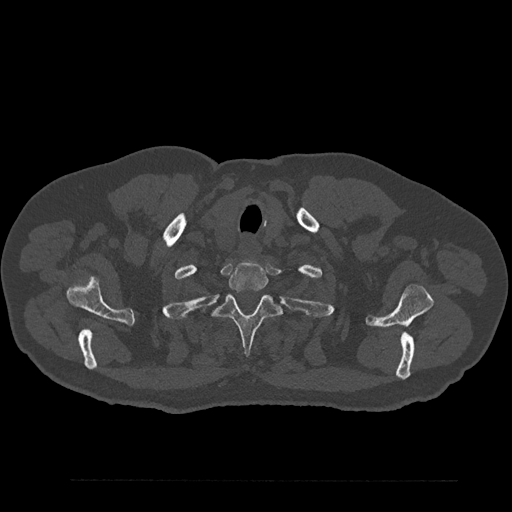
CT including the spine, one axial slice; slice 727 of 797 in the series (ordered by position); reconstruction kernel Br40s/3; 120 kVp; bone window (W 1800 / L 400 HU); 0.5 mm slice thickness; 512 × 512 image matrix. Patient: male, 61 years. Case-level facts recorded for this patient, not image findings: primary cancer: prostate.
Annotated regions visible in this slice (semi-automatic segmentation, software-assisted and operator-edited):
- T1 vertebra: bounding box [x1, y1, x2, y2] px = [228, 262, 268, 292]
- T2 vertebra: [214, 295, 281, 355]